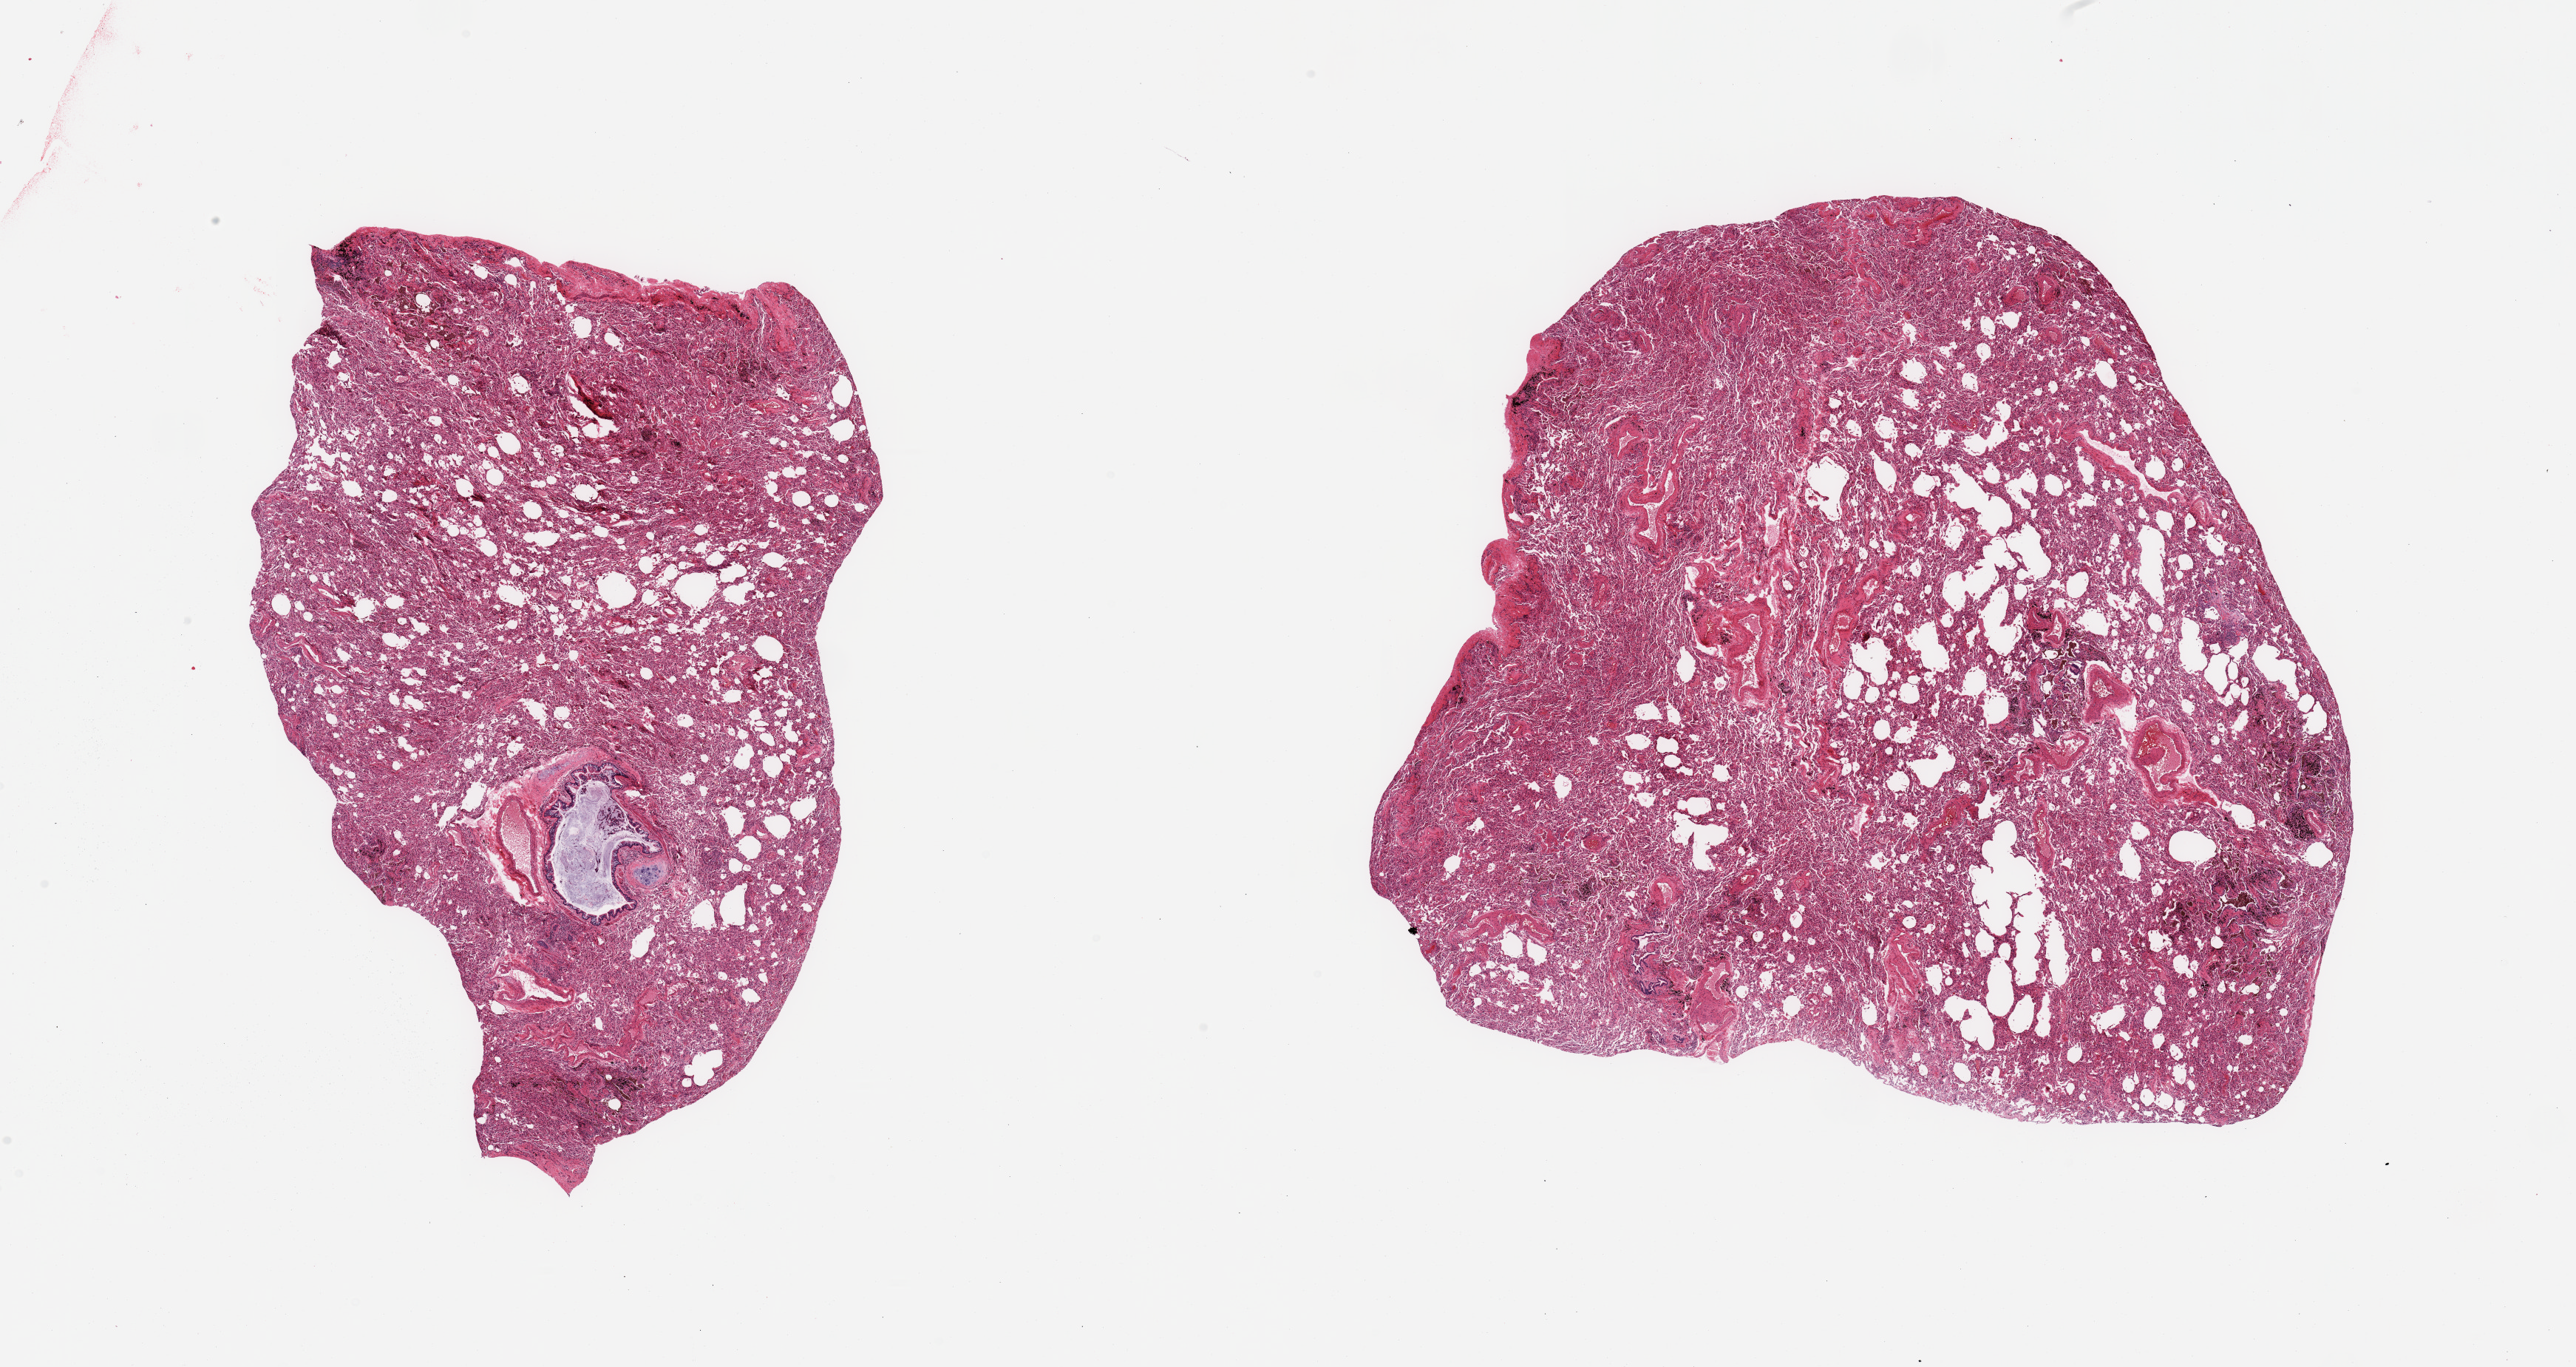
Haematoxylin and eosin whole-slide image, whole scanned area (about 27.6 x 14.6 mm, slide scanned at 20x) shown as a low-resolution overview; PAXgene-fixed paraffin-embedded (PFPE) section; sampled site (target tissue): lung; tissue donor sample. Male donor.
Pathologist's review note for this sample: 2 pieces, mild congestion; moderate atelectasis; well-preserved intermediate bronchus.